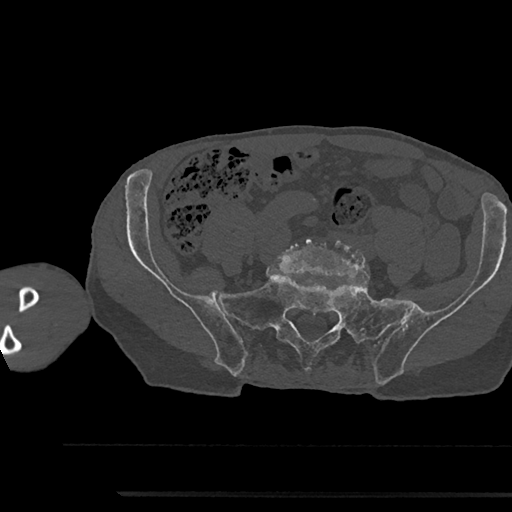
CT including the spine, one axial slice. Position 303 of 797 along the scan axis. Reconstruction kernel Br40s/3. 120 kVp. Bone window (W 1800 / L 400 HU). 512 × 512 image matrix, field of view 367 × 367 mm. Patient: male, 79 years. Case-level facts recorded for this patient, not image findings: primary cancer: prostate.
Annotated regions visible in this slice (semi-automatic segmentation, software-assisted and operator-edited):
- L5 vertebra: bounding box [x1, y1, x2, y2] px = [278, 235, 370, 279]